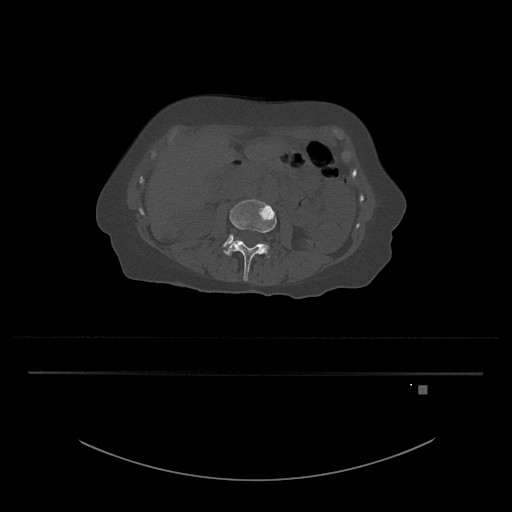
CT including the spine, one axial slice; position 416 of 797 along the scan axis; bone window (W 1800 / L 400 HU); 512 × 512 image matrix. Patient: female, 57 years. From the clinical record (not read from this slice): primary cancer: cervical.
Outlined on this slice (semi-automatically segmented with operator editing):
- L3 vertebra: box from (x=223, y=199) to (x=277, y=281) px
- L4 vertebra: (x=223, y=234)–(x=269, y=257)